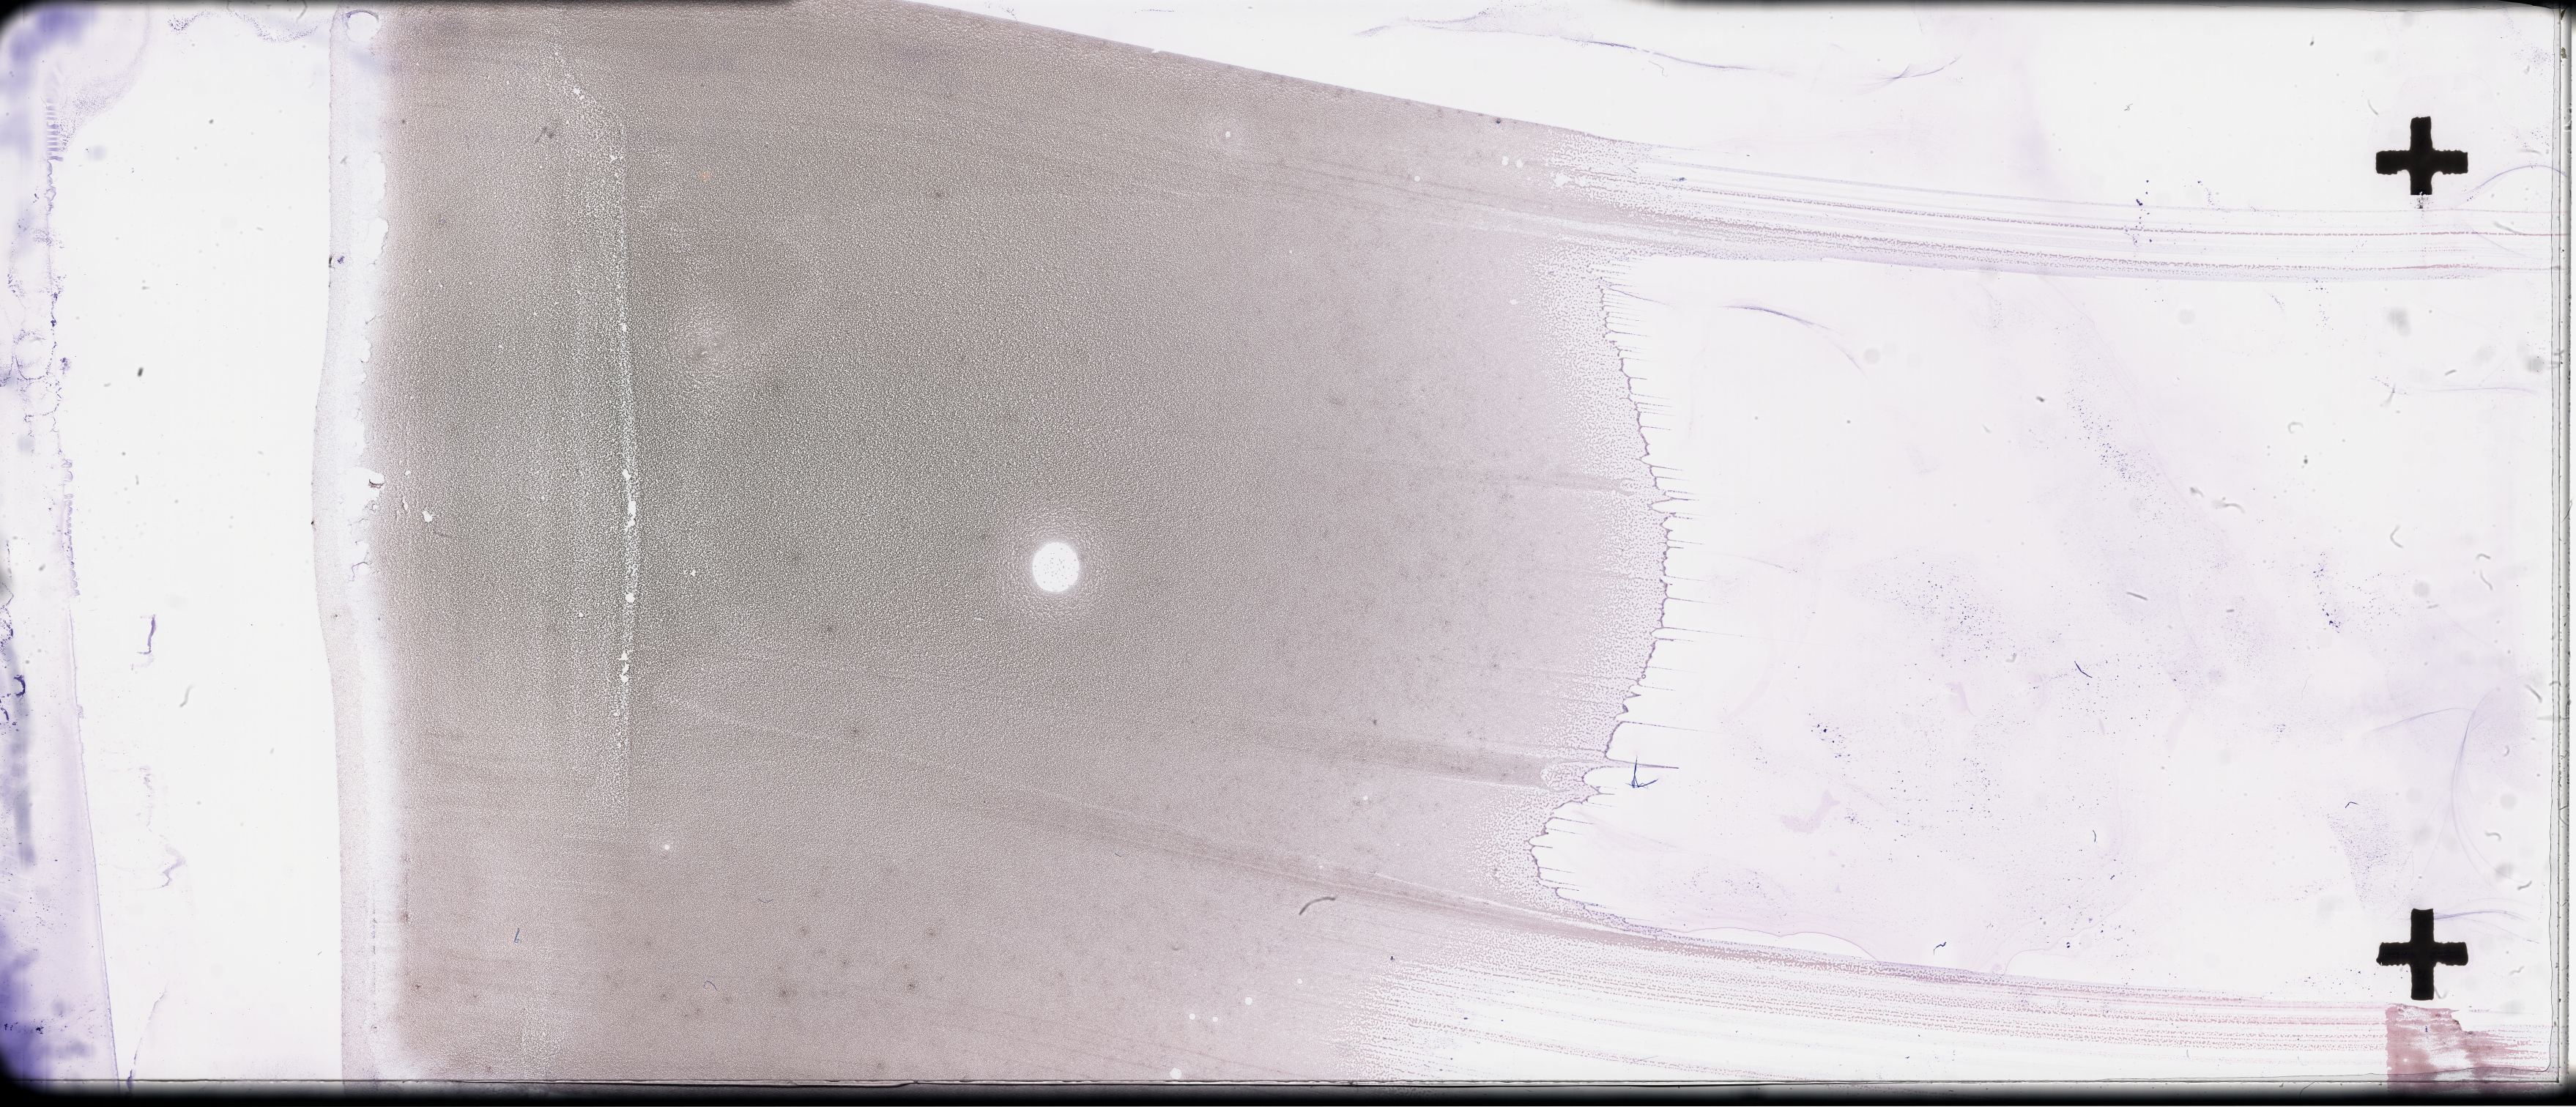
Whole-slide image of a whole blood smear, Wright-Giemsa stain, low-resolution overview of the scanned area, about 56.8 x 24.4 mm, EDTA-anticoagulated smear. Female patient.
Patient diagnosis: Plasma Cell Myeloma.